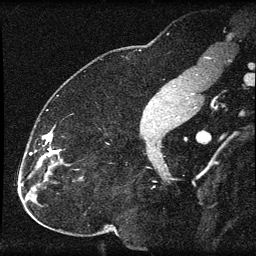
Breast MRI (dynamic contrast-enhanced), one sagittal slice. Position 31 of 60 along the scan axis. Dynamic contrast-enhanced series, image 2 of 3 at this slice position (ordered by acquisition). 1.5 T. TE 4.2 ms, TR 8.2 ms. 2 mm slice thickness. 256 × 256 image matrix, field of view 180 × 180 mm. Patient: female, 32 years.
Annotated regions visible in this slice (semi-automatic segmentation, software-assisted and operator-edited):
- analysis volume of interest (the breast-tissue region the enhancement analysis was run in; not a lesion): bounding box <31,129,68,184> (left, top, right, bottom; pixels)
- tumour enhancement mask (voxels above the 70 % enhancement threshold inside the analysis volume of interest): <43,135,58,156>